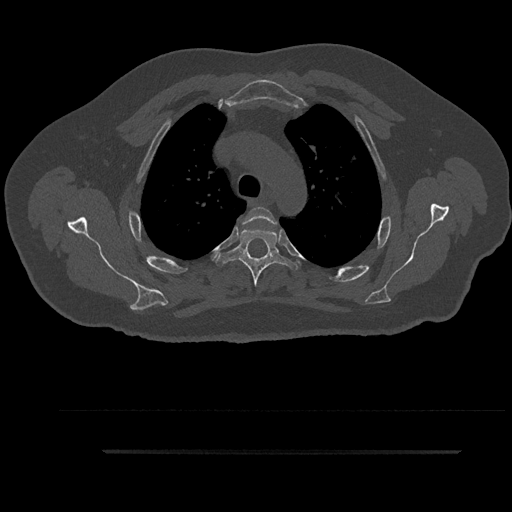
CT including the spine, one axial slice. Slice 681 of 797 in the series (ordered by position). Reconstruction kernel Br40s/3. Bone window (W 1800 / L 400 HU). 0.5 mm slice thickness. 512 × 512 image matrix. Male patient, age 63 years. Case-level facts recorded for this patient, not image findings: primary cancer: renal.
Outlined on this slice (semi-automatically segmented with operator editing):
- T3 vertebra: bounding box [x1, y1, x2, y2] px = [243, 207, 277, 225]
- T4 vertebra: [215, 228, 299, 287]